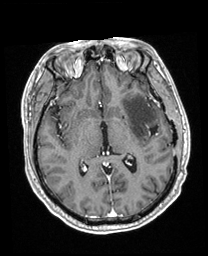
Brain MRI from a brain-tumour surgery series, one axial slice; position 109 of 208 along the scan axis; T1-weighted post-contrast; 1 mm slice thickness; 208 × 256 image matrix, field of view 211 × 260 mm. Case-level facts recorded for this patient, not image findings: histopathology: Astrocytoma; WHO grade: 3.
Structures marked on this image (manually delineated by an expert):
- previous resection cavity: box from (x=150, y=126) to (x=158, y=136) px